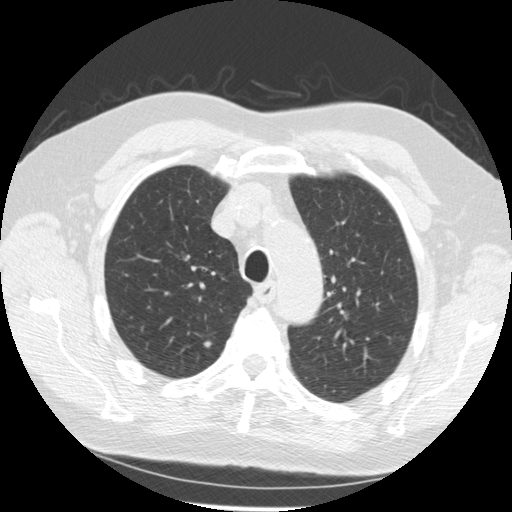
Low-dose screening chest CT, one axial slice. Slice 204 of 259 in the series (ordered by position). Reconstruction kernel STANDARD. Lung window (W 1500 / L -600 HU). 2.5 mm slice thickness. 512 × 512 image matrix, field of view 355 × 355 mm.
Annotated regions visible in this slice (expert manual segmentation):
- lesion 1 (nodule, upper lobe of right lung): box from (x=203, y=340) to (x=213, y=348) px